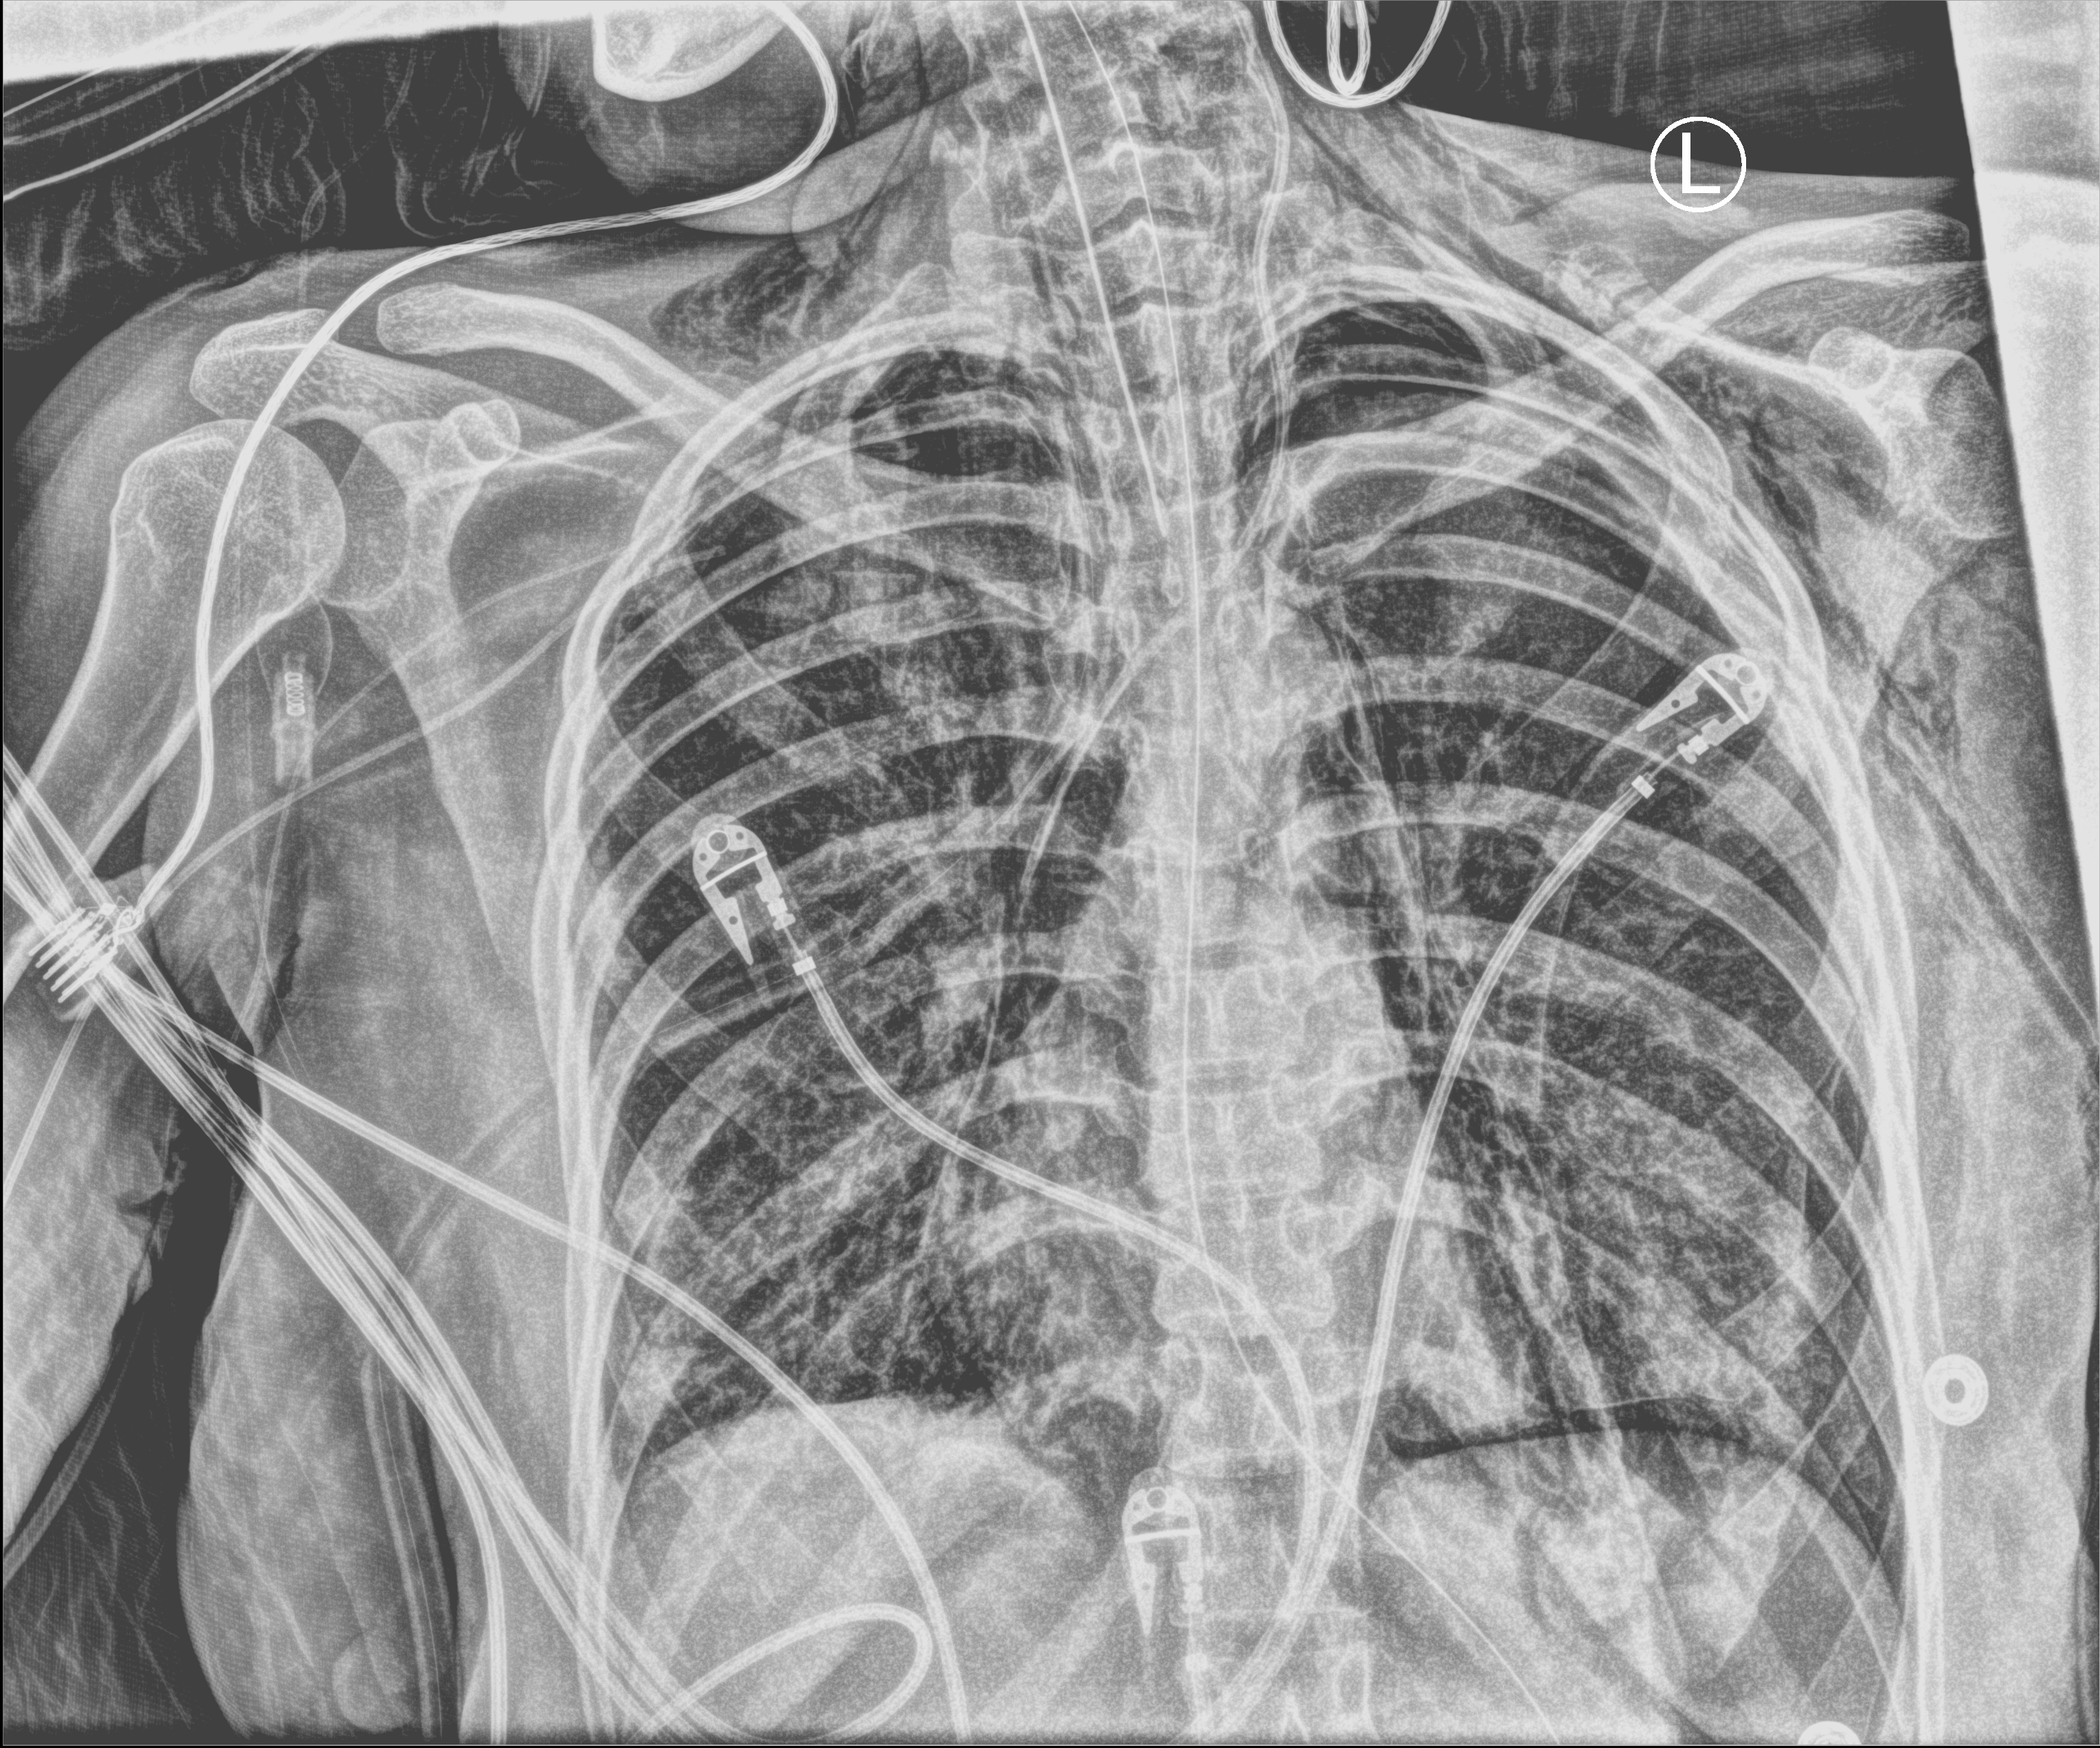
Portable chest radiograph, anteroposterior (AP) projection. Adult patient hospitalised with COVID-19, age 18–59 years.
From the hospital-stay record, not from the radiograph (when in the stay this image was taken is not recorded): smoking status (admission record): never.